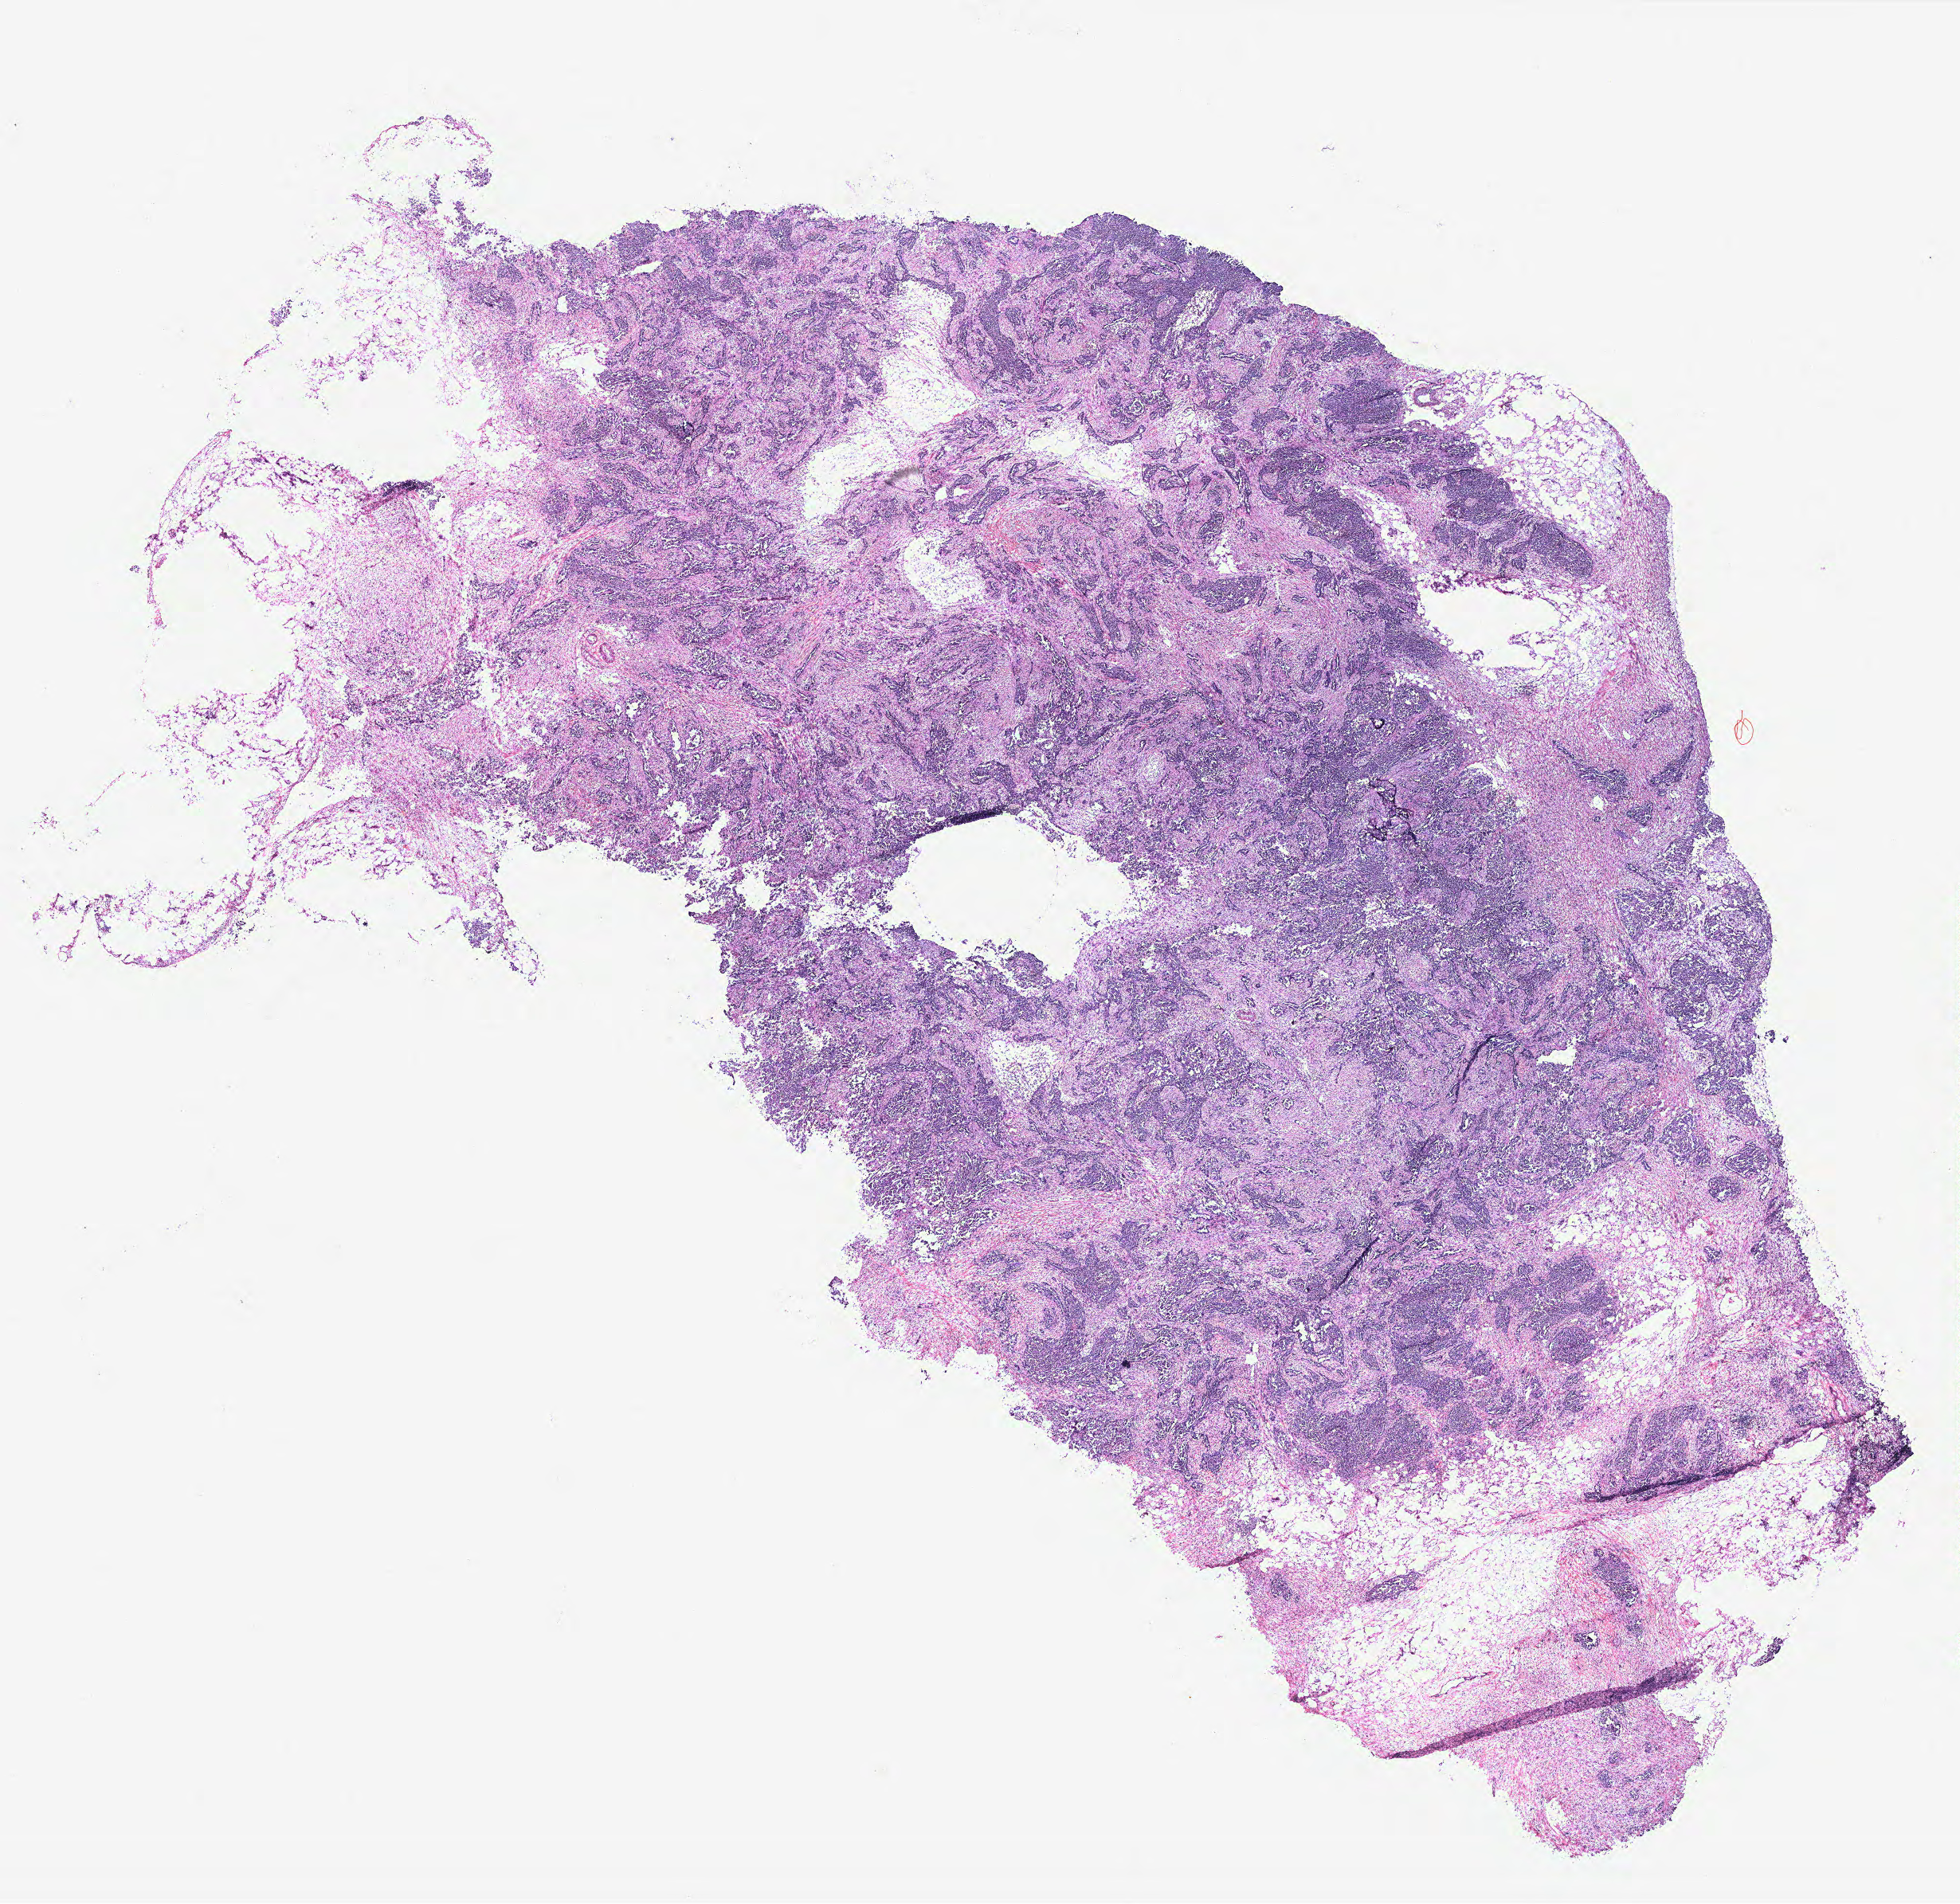
Digitized Hematoxylin and eosin (H&E) stained tissue section (whole slide) — a low-resolution overview of the entire scanned area, about 19.7 x 19.1 mm. Tumour tissue sample, ovary. Female, 62 y/o.
Histologic diagnosis: Serous adenocarcinoma, NOS.